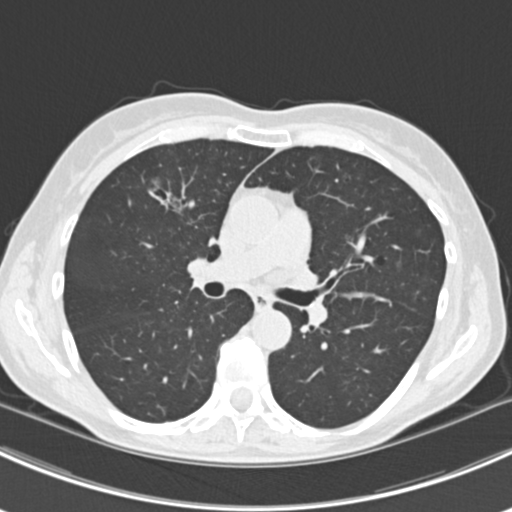
Axial slice from a low-dose chest CT screening exam; baseline screening round; lung window (W 1500 / L -600 HU); 2 mm slice thickness; 512 × 512 image matrix. Female participant, aged 63 years at enrolment. Current smoker at enrolment.
• Lesion marked by an expert reader, bounding box [x1, y1, x2, y2] px = [145, 173, 202, 228].
• The screening reader recorded 10 non-calcified nodules or masses ≥4 mm on this exam (right lower lobe, right lower lobe, left lower lobe, left lower lobe, right middle lobe, right lower lobe, left lower lobe, left upper lobe, right upper lobe, left upper lobe); which of them this box marks is not recorded.
• Participant outcome: lung cancer diagnosed 751 days after this screen (after the third annual screen) — bronchiolo-alveolar adenocarcinoma, NOS, right upper lobe, right middle lobe, right lower lobe, left upper lobe, left lower lobe, moderately differentiated (G2), stage IV (AJCC 6th edition).